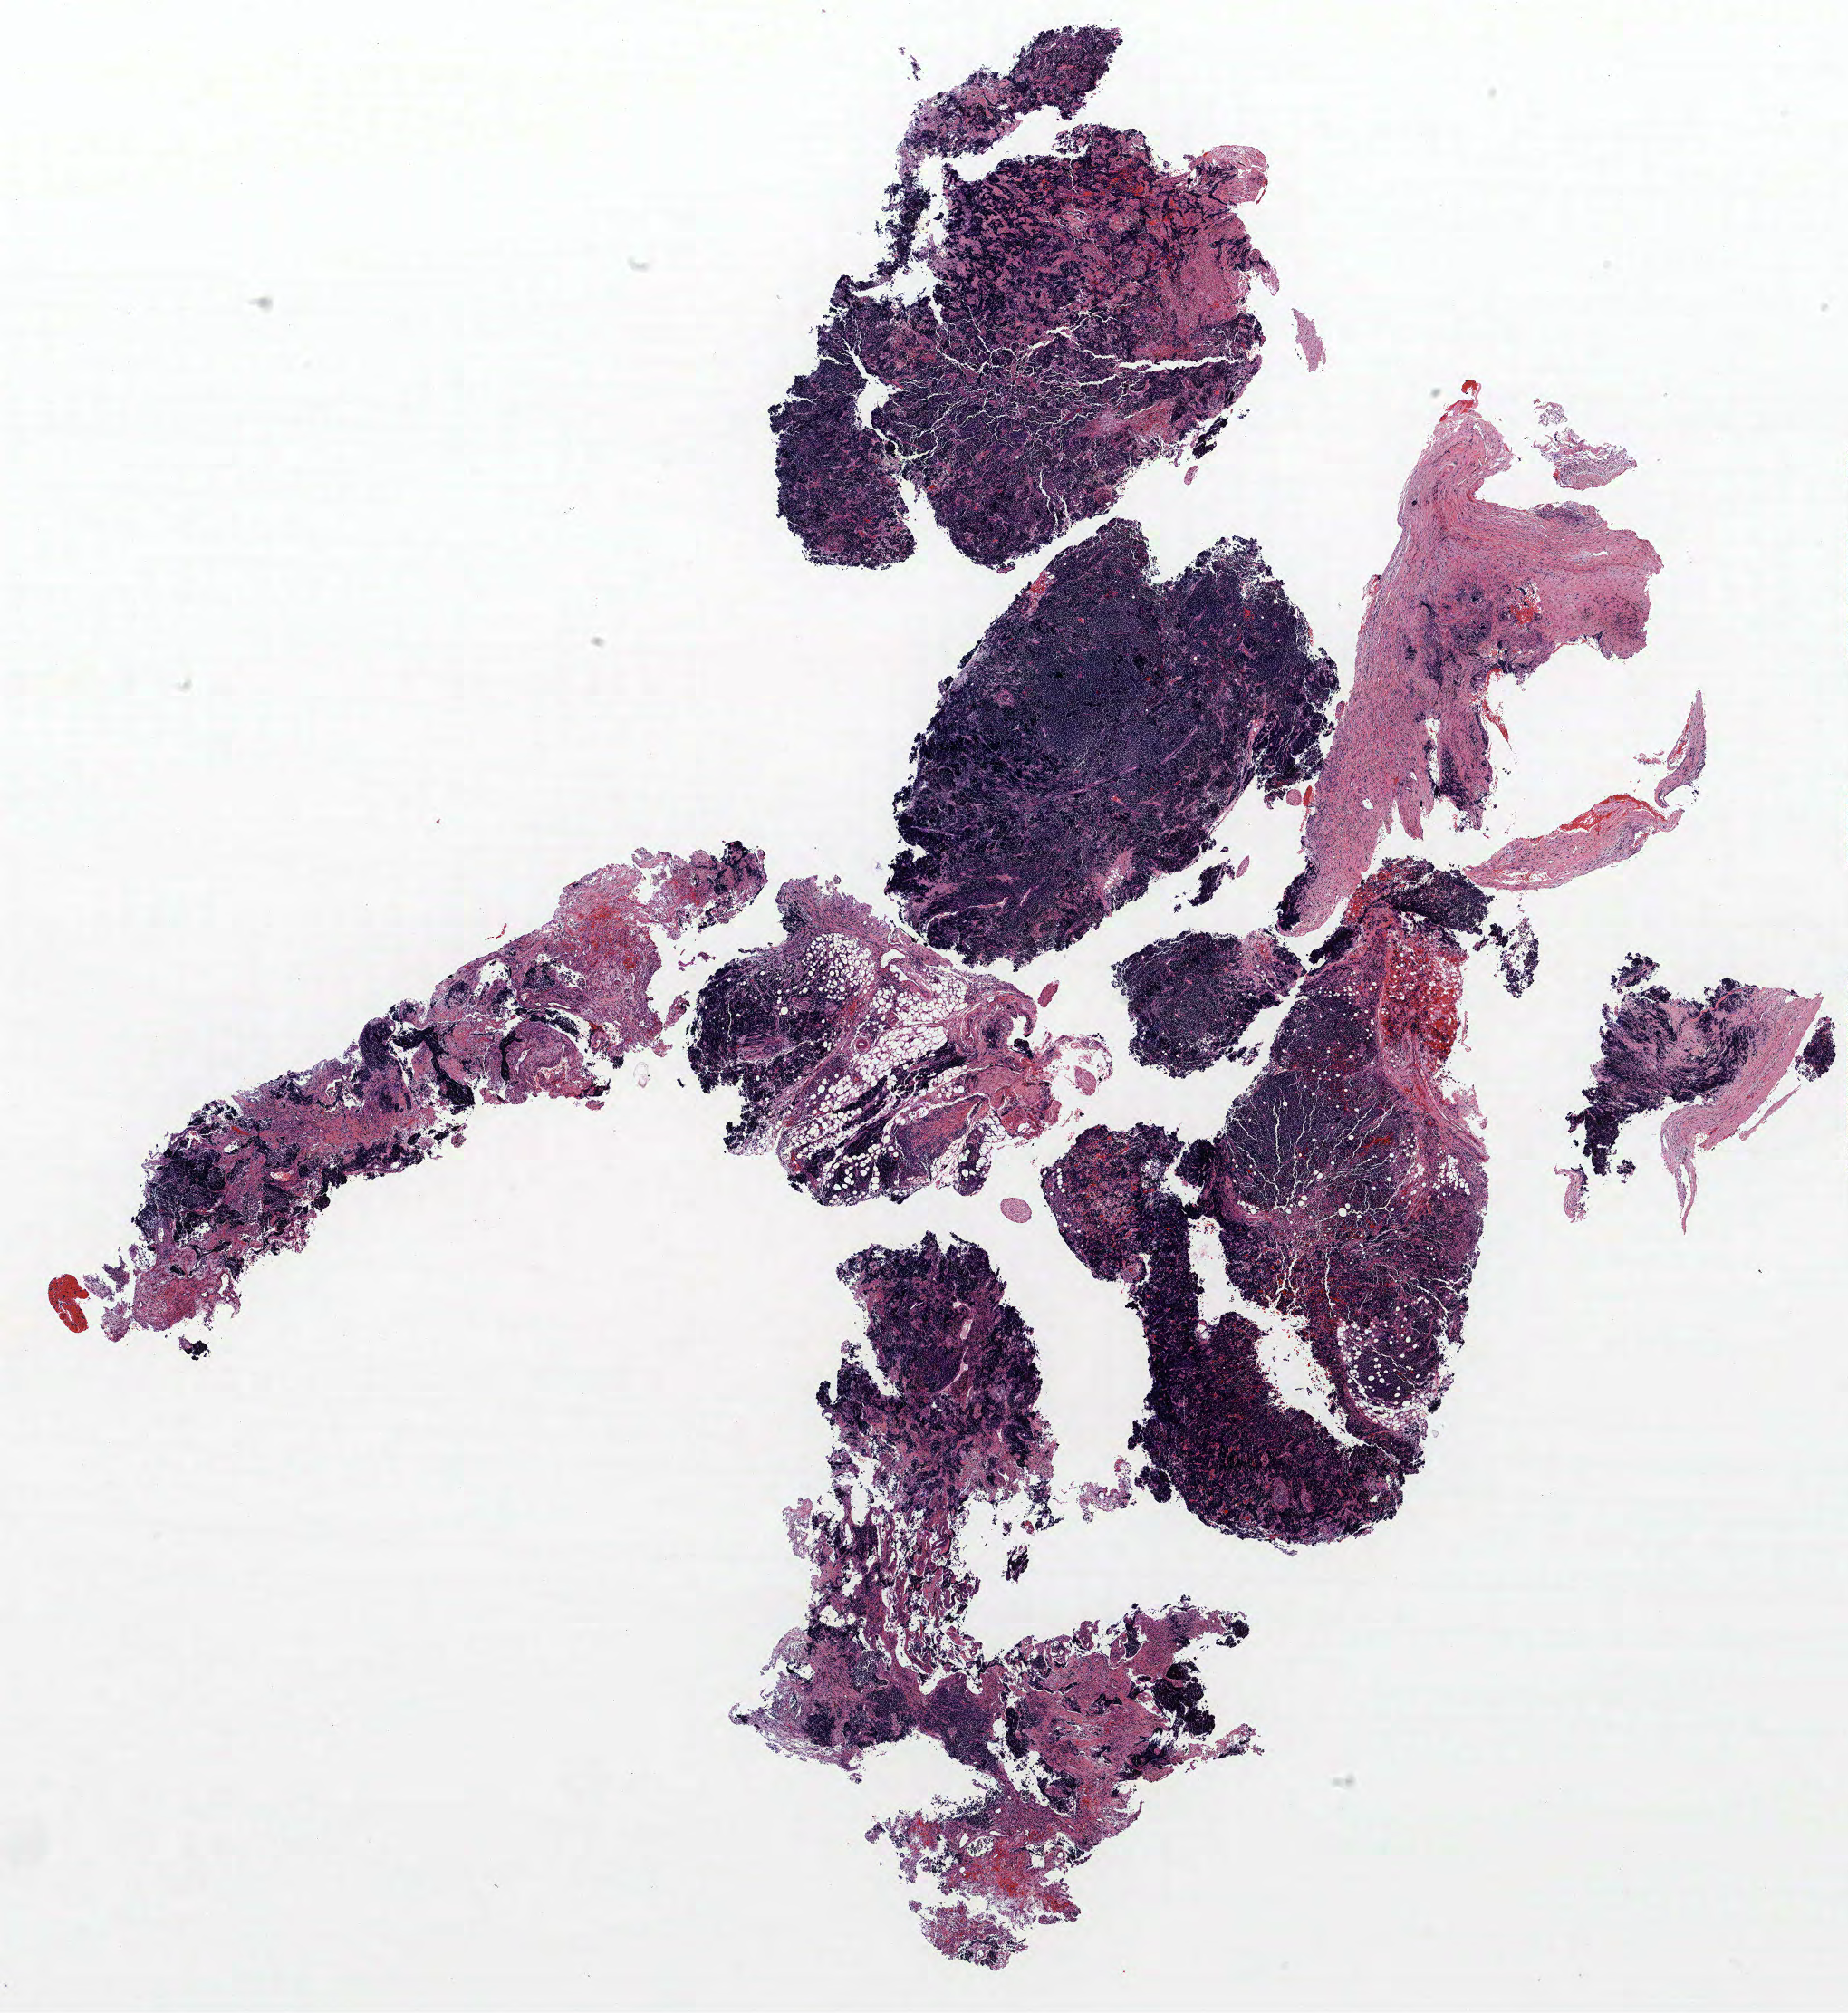
Whole-slide histology image, Hematoxylin and eosin (H&E) stained, low-resolution overview of the scanned area, about 16.3 x 17.8 mm (from a 40x scan). FFPE section. Lung tissue. Female, age 64 at enrolment. Grade: cannot be assessed (GX).
Participant's lung-cancer diagnosis: Small cell carcinoma, NOS. Tumour size (pathology): 12 mm. Primary tumour location (clinical record): right upper lobe. Stage (AJCC 6th edition): IV.